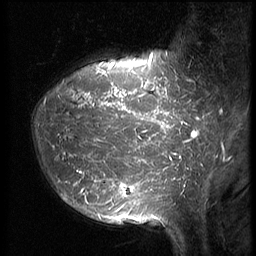
Breast MRI (dynamic contrast-enhanced), one sagittal slice. Slice 16 of 64 in the series (ordered by position). 3 images stored at this slice position (order not interpretable as contrast timing). 1.5 T. TE 4.2 ms, TR 9 ms. 256 × 256 image matrix. Female patient, age 39 years. From the clinical record (not read from this slice): setting: breast cancer imaged before/during neoadjuvant chemotherapy; receptor status: HER2-positive.
Structures marked on this image (semi-automatic segmentation, software-assisted and operator-edited):
- analysis volume of interest (the breast-tissue region the enhancement analysis was run in; not a lesion): bounding box [x1, y1, x2, y2] px = [31, 47, 210, 239]
- tumour enhancement mask (voxels above the 140 % enhancement threshold inside the analysis volume of interest): [59, 53, 210, 217]